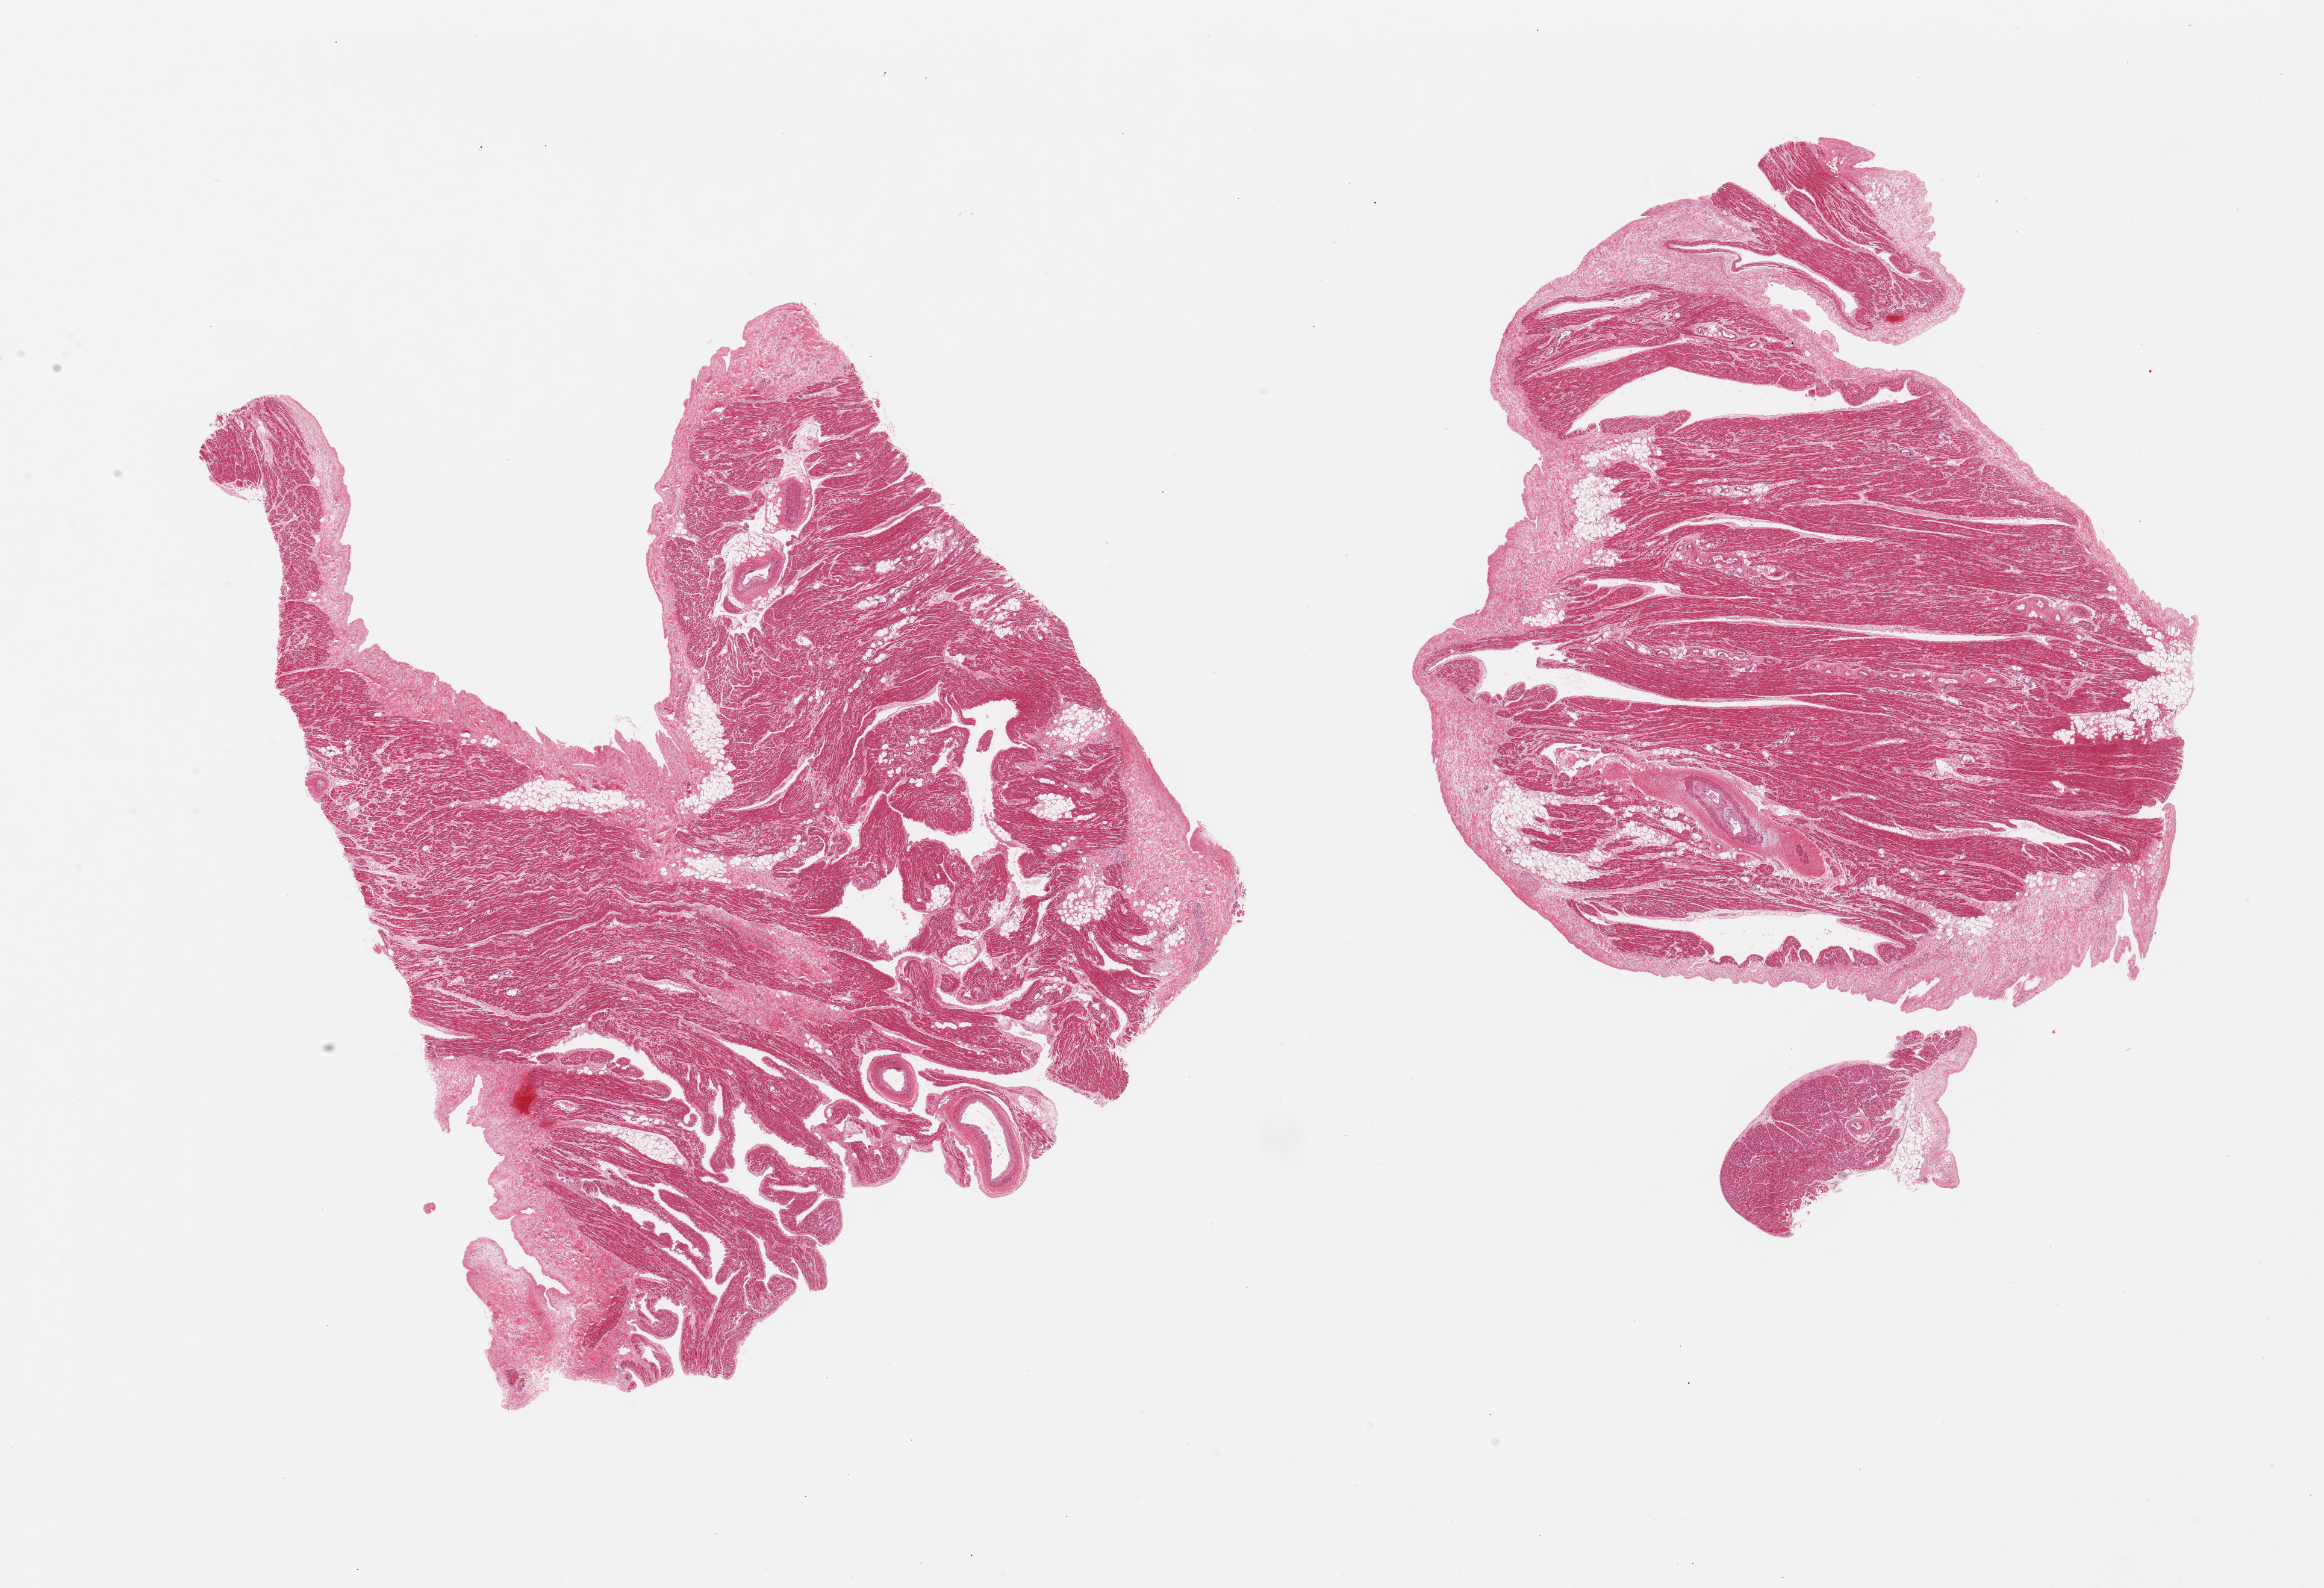
Haematoxylin and eosin whole-slide image — a low-resolution overview of the entire scanned area, about 30.5 x 20.9 mm, PAXgene-fixed, paraffin-embedded tissue, sampled site (target tissue): auricular appendage, tissue donor sample. Donor: female.
Reviewer comment on this tissue sample: 2 pieces, no abnormalities.